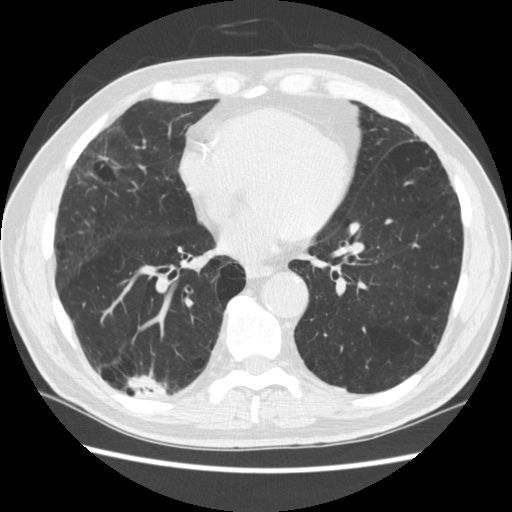
Low-dose screening chest CT, one axial slice; slice 113 of 266 in the series (ordered by position); lung window (W 1500 / L -600 HU); 512 × 512 image matrix, field of view 360 × 360 mm.
Outlined on this slice (expert manual segmentation):
- lesion 1 (tumor, upper lobe of right lung): bounding box <129,376,167,398> (left, top, right, bottom; pixels)